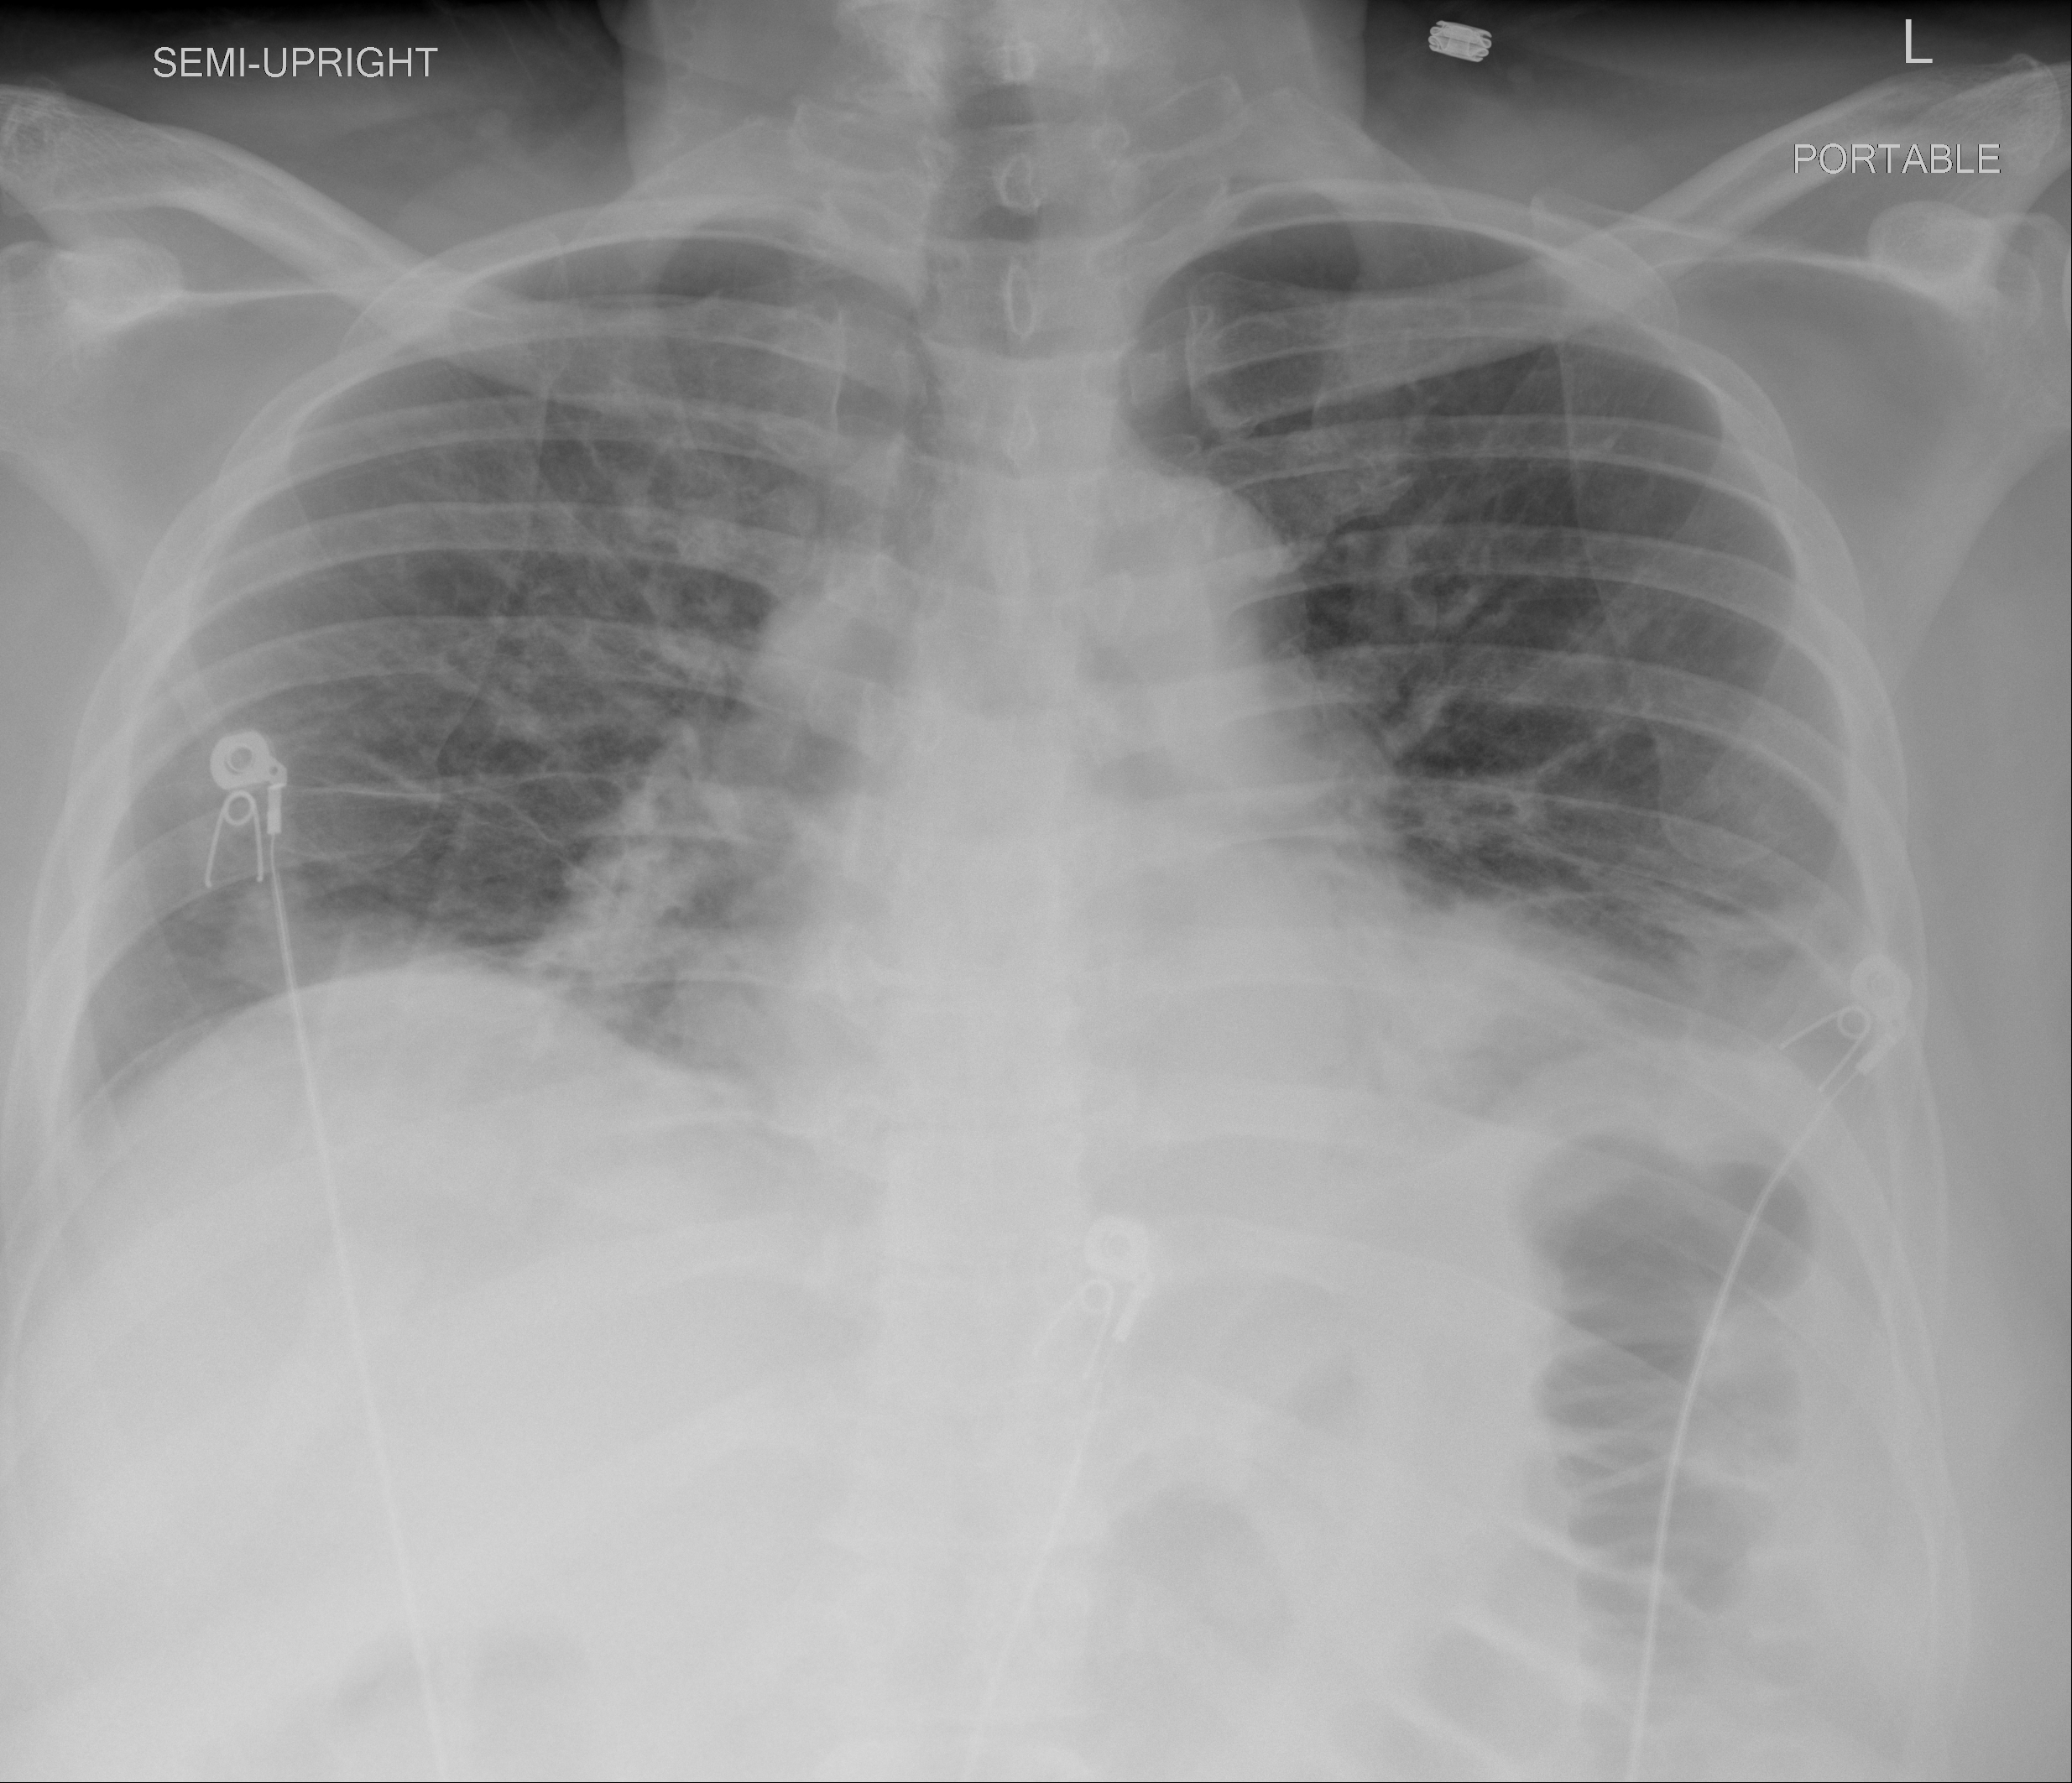
Chest X-ray (portable), AP projection. Female patient, age 57 years; COVID-19 (test-positive).
Radiologist's key findings for this exam: streaky opacities mainly in the lung bases near the hemidiaphragms. Increased somewhat patchy opacities are now seen in both lung bases more conspicuous compared to the prior studies.